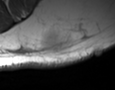
MRI of an extremity soft-tissue mass, one axial slice. Position 26 of 35 along the scan axis. MR volume resampled by the dataset authors to the PET/CT grid (not the native acquisition matrix). 3.27 mm slice thickness. 115 × 90 image matrix, field of view 112 × 88 mm. Male patient. Case-level facts recorded for this patient, not image findings: histological type: pleiomorphic leiomyosarcoma; grade: high; site of the primary tumour: left buttock.
Structures marked on this image (expert contour drawn on MRI and transferred to this co-registered scan by the dataset authors):
- gross tumour volume including surrounding oedema: bounding box [x1, y1, x2, y2] px = [42, 30, 61, 56]
- gross tumour volume (mass): [44, 34, 61, 54]